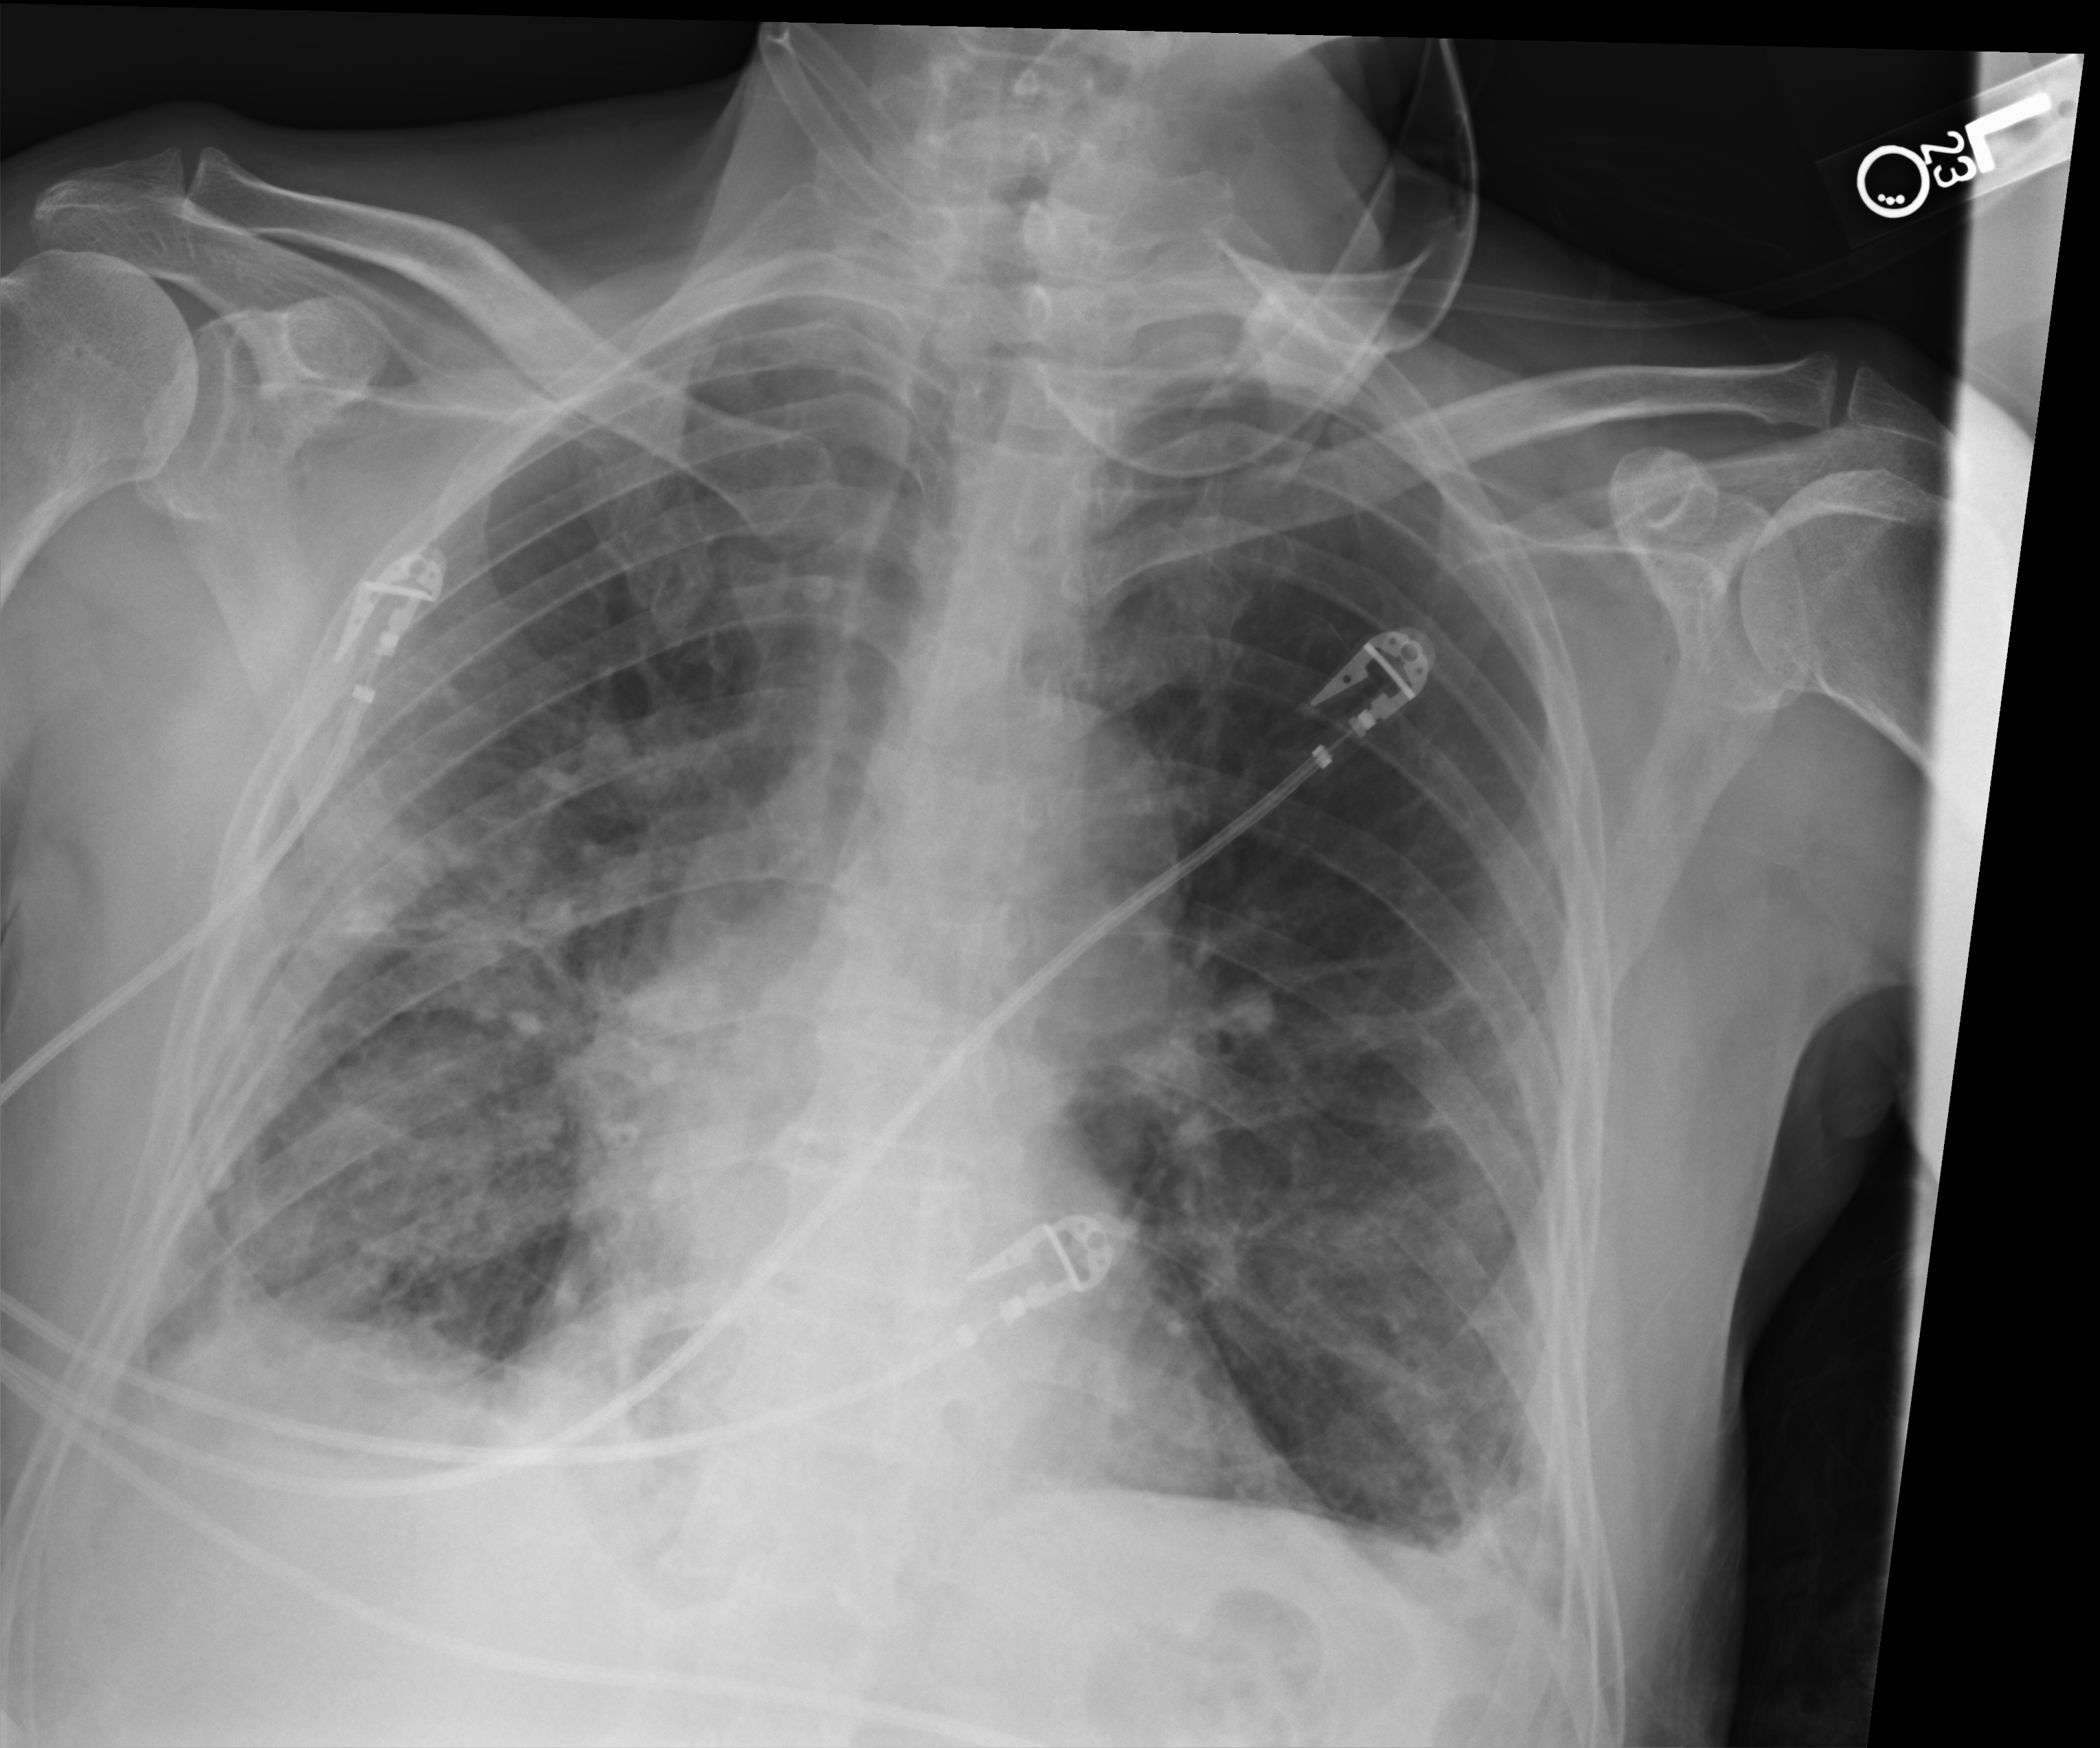
Portable chest radiograph; anteroposterior (AP) projection. Male patient hospitalised with COVID-19, age 75–90 years.
Admission-level facts for this patient (not findings on this image; timing relative to this image not recorded):
- admitted to intensive care during this hospital stay: yes